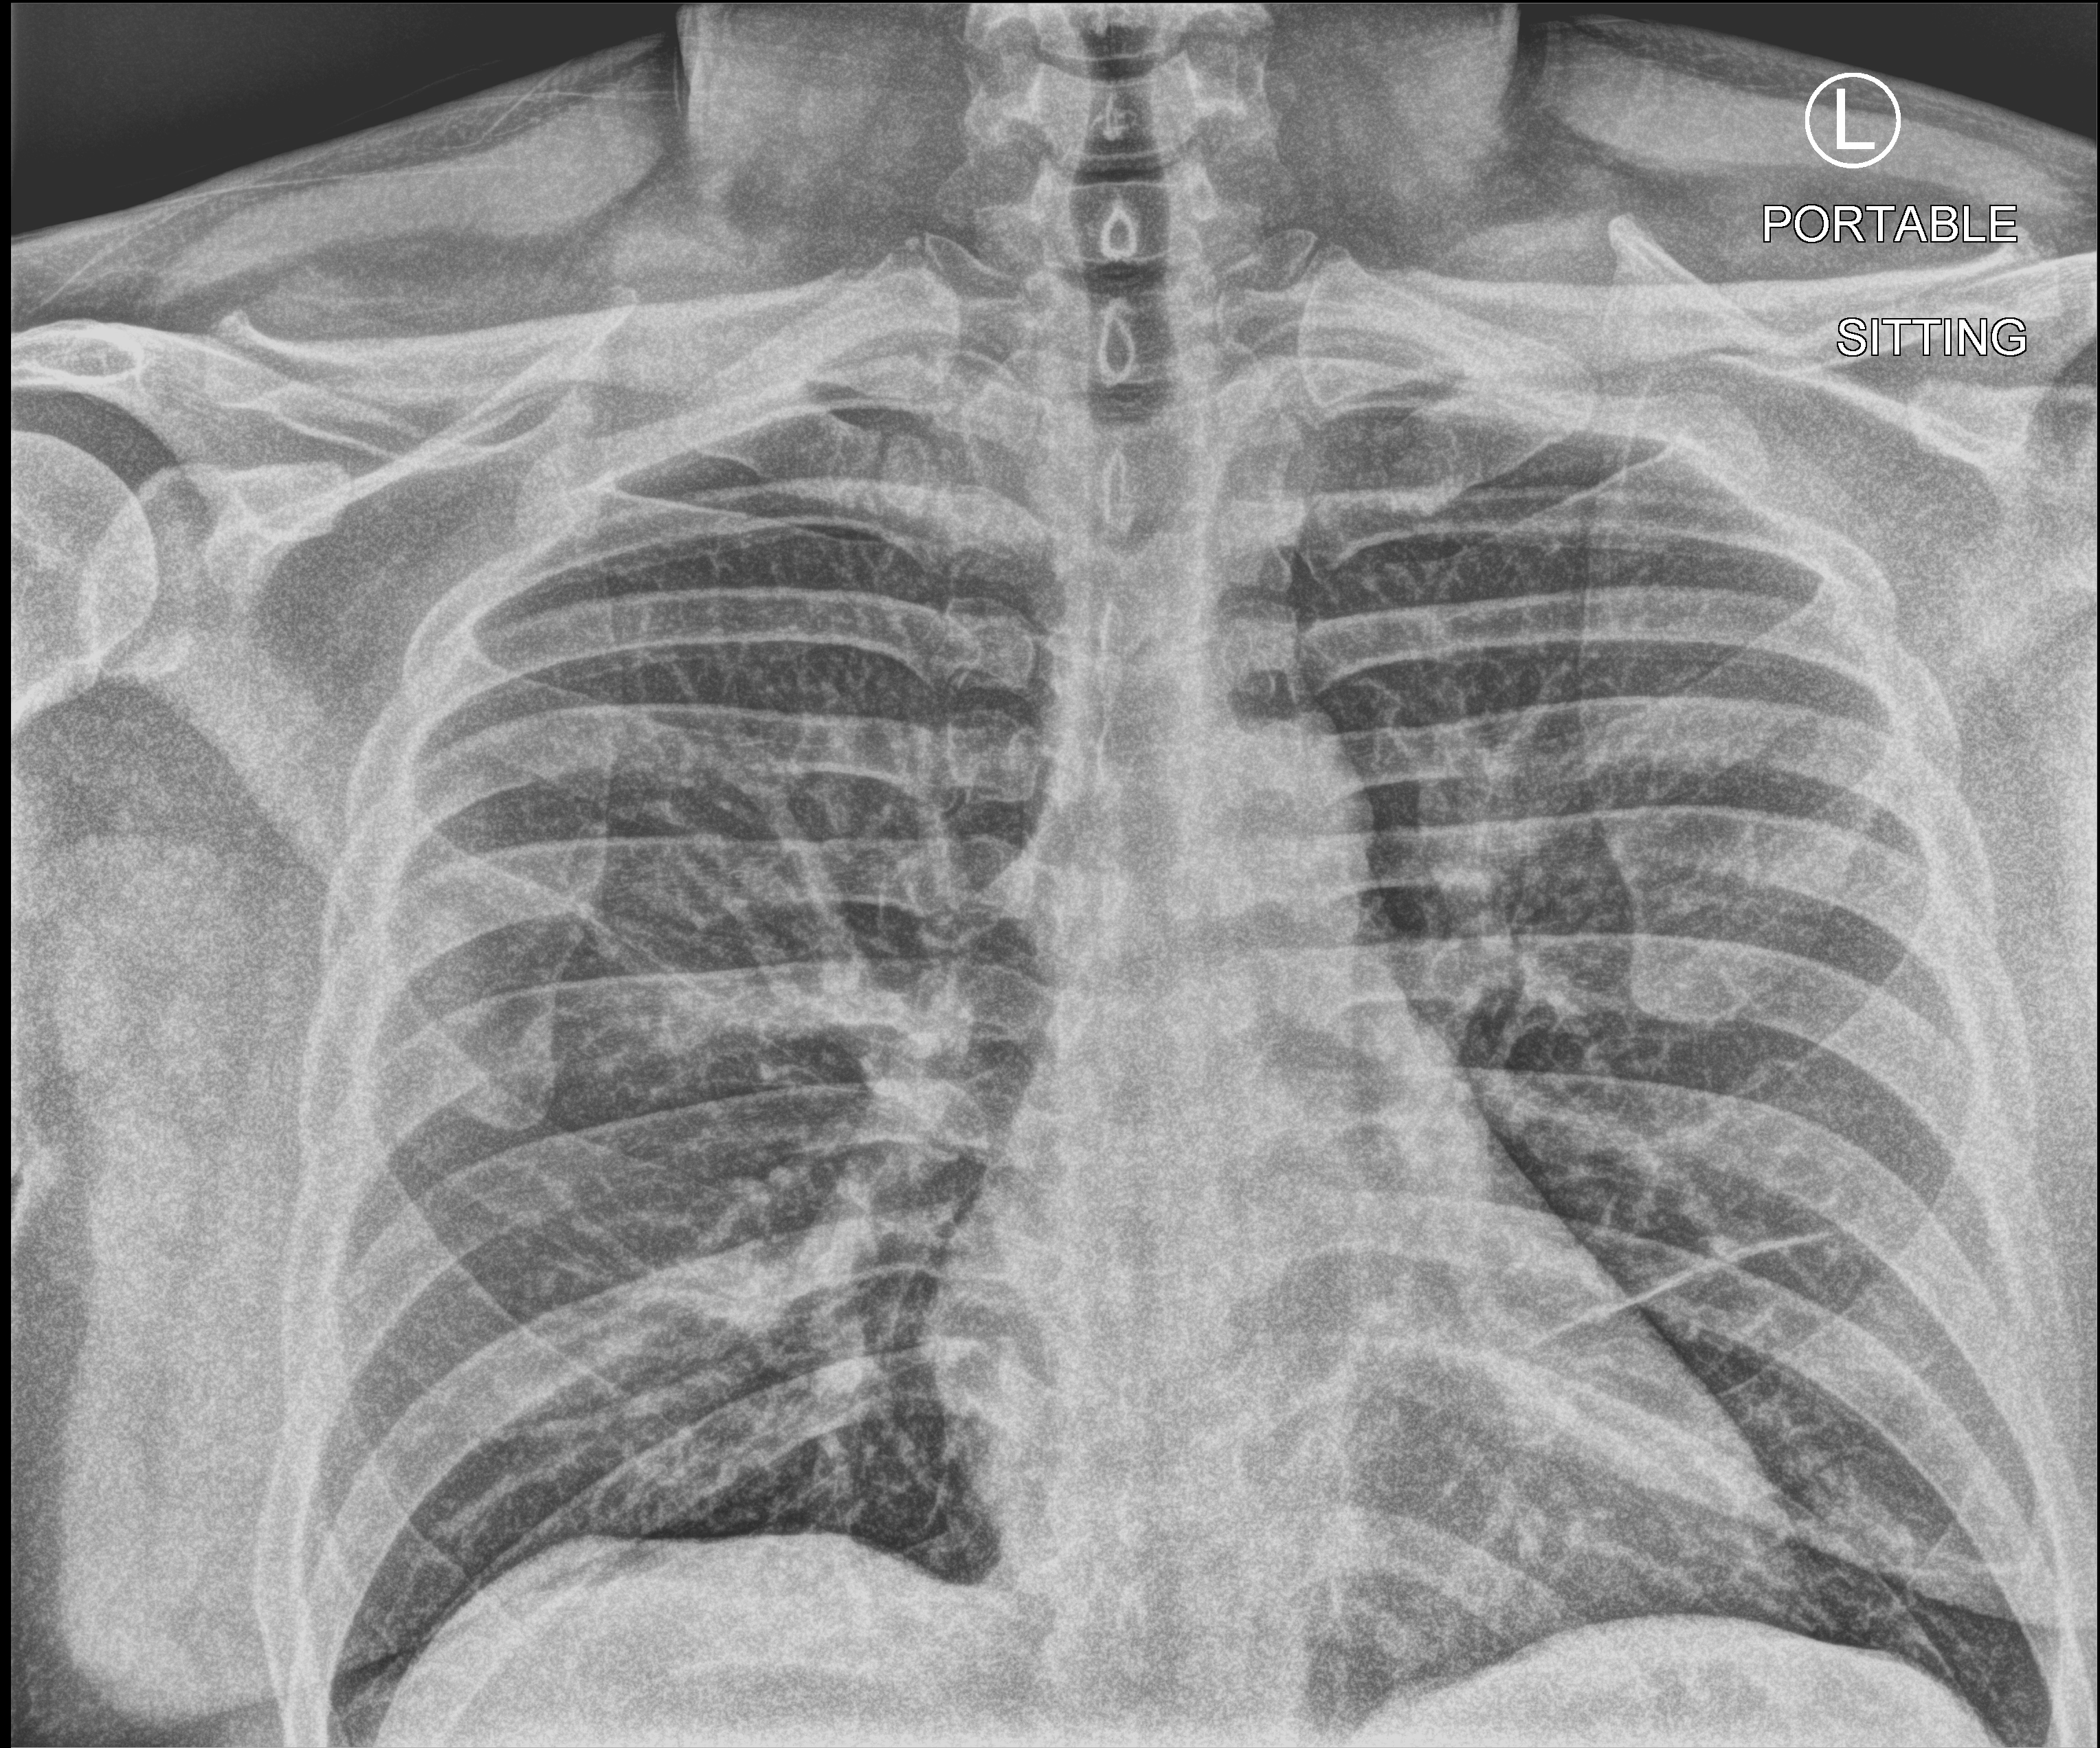
Bedside chest radiograph (computed radiography); anteroposterior (AP) projection. Patient hospitalised with COVID-19; male, aged 18–59 years.
Hospital-stay facts (about this admission, not read from this image; timing relative to this image not recorded):
- mechanically ventilated during this hospital stay: no